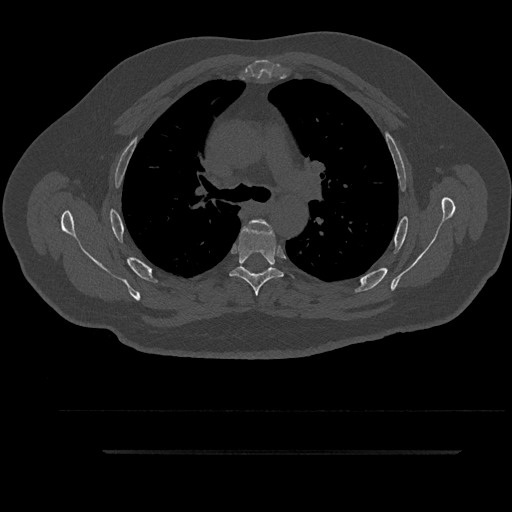
CT including the spine, one axial slice; position 630 of 797 along the scan axis; reconstruction kernel Br40s/3; 120 kVp; bone window (W 1800 / L 400 HU); 512 × 512 image matrix, field of view 432 × 432 mm. Patient: male, 63 years. From the clinical record (not read from this slice): primary cancer: renal; vertebrae with lytic lesions (as recorded): T8.
Annotated regions visible in this slice (semi-automatically segmented with operator editing):
- T4 vertebra: bounding box [x1, y1, x2, y2] px = [248, 219, 272, 228]
- T5 vertebra: [229, 221, 285, 296]
- T6 vertebra: [260, 268, 269, 274]